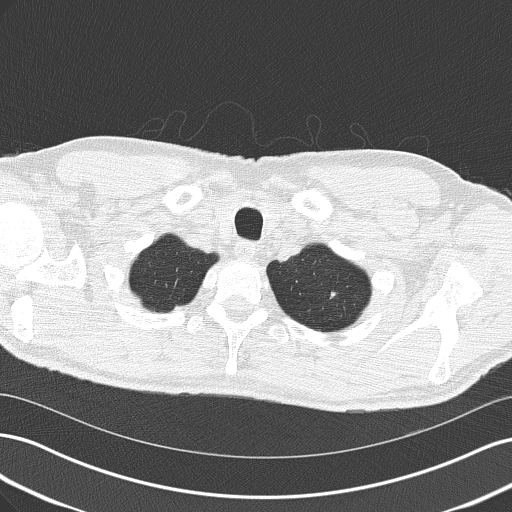
Low-dose screening chest CT, axial slice. Second annual screen. Lung window (W 1500 / L -600 HU). 2 mm slice thickness. Lung (sharp) reconstruction kernel (B50f). 140 kVp. 512 × 512 image matrix. Male participant, aged 64 years at enrolment.
- Expert reader's lesion annotation, bounding box (x1, y1, x2, y2) in pixels: (315, 279, 350, 309).
- The screening reader recorded 2 non-calcified nodules or masses ≥4 mm on this exam (left upper lobe, left upper lobe); which of them this box marks is not recorded.